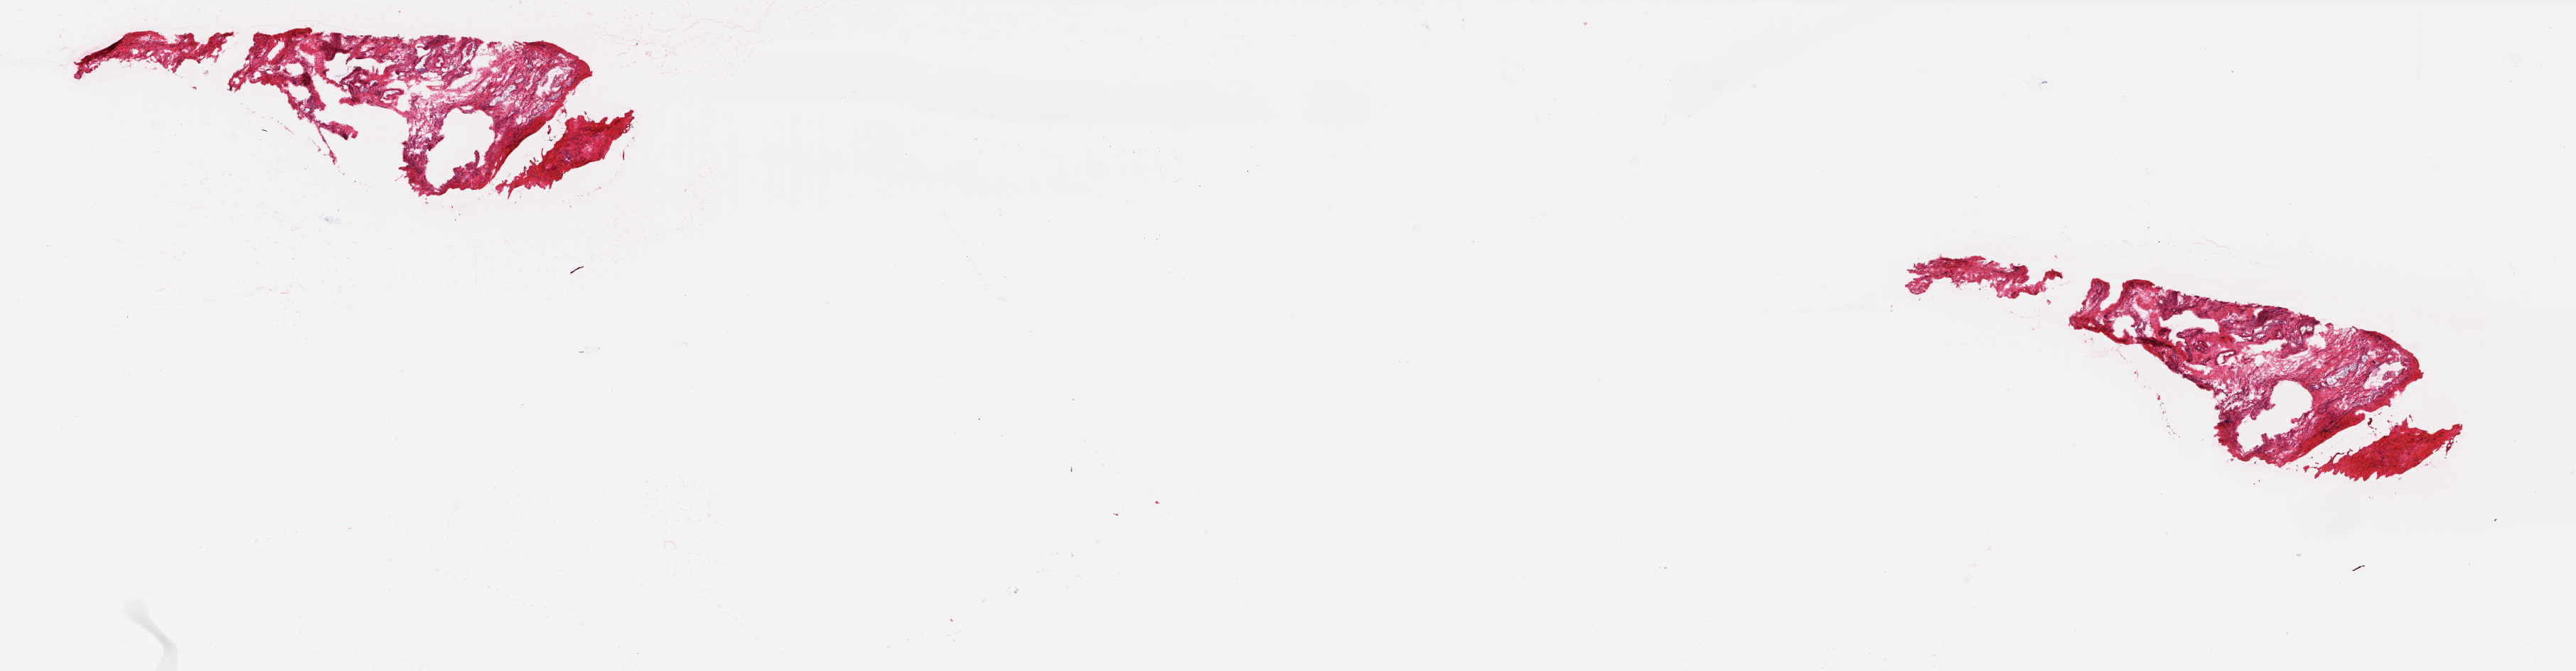
H&E whole-slide image — whole scanned area (about 28.9 x 7.5 mm) shown as a low-resolution overview, frozen section, sample: primary tumour, ovary. Female patient; age at initial diagnosis 52 years. Histologic grade: G3 (poorly differentiated). Pathologist review of this section (percent, as recorded): tumour cells 50%, tumour nuclei 70%, normal cells 0%, stromal cells 50%, necrosis 0%.
- pathologic diagnosis: Serous cystadenocarcinoma, NOS
- FIGO stage: IIIB